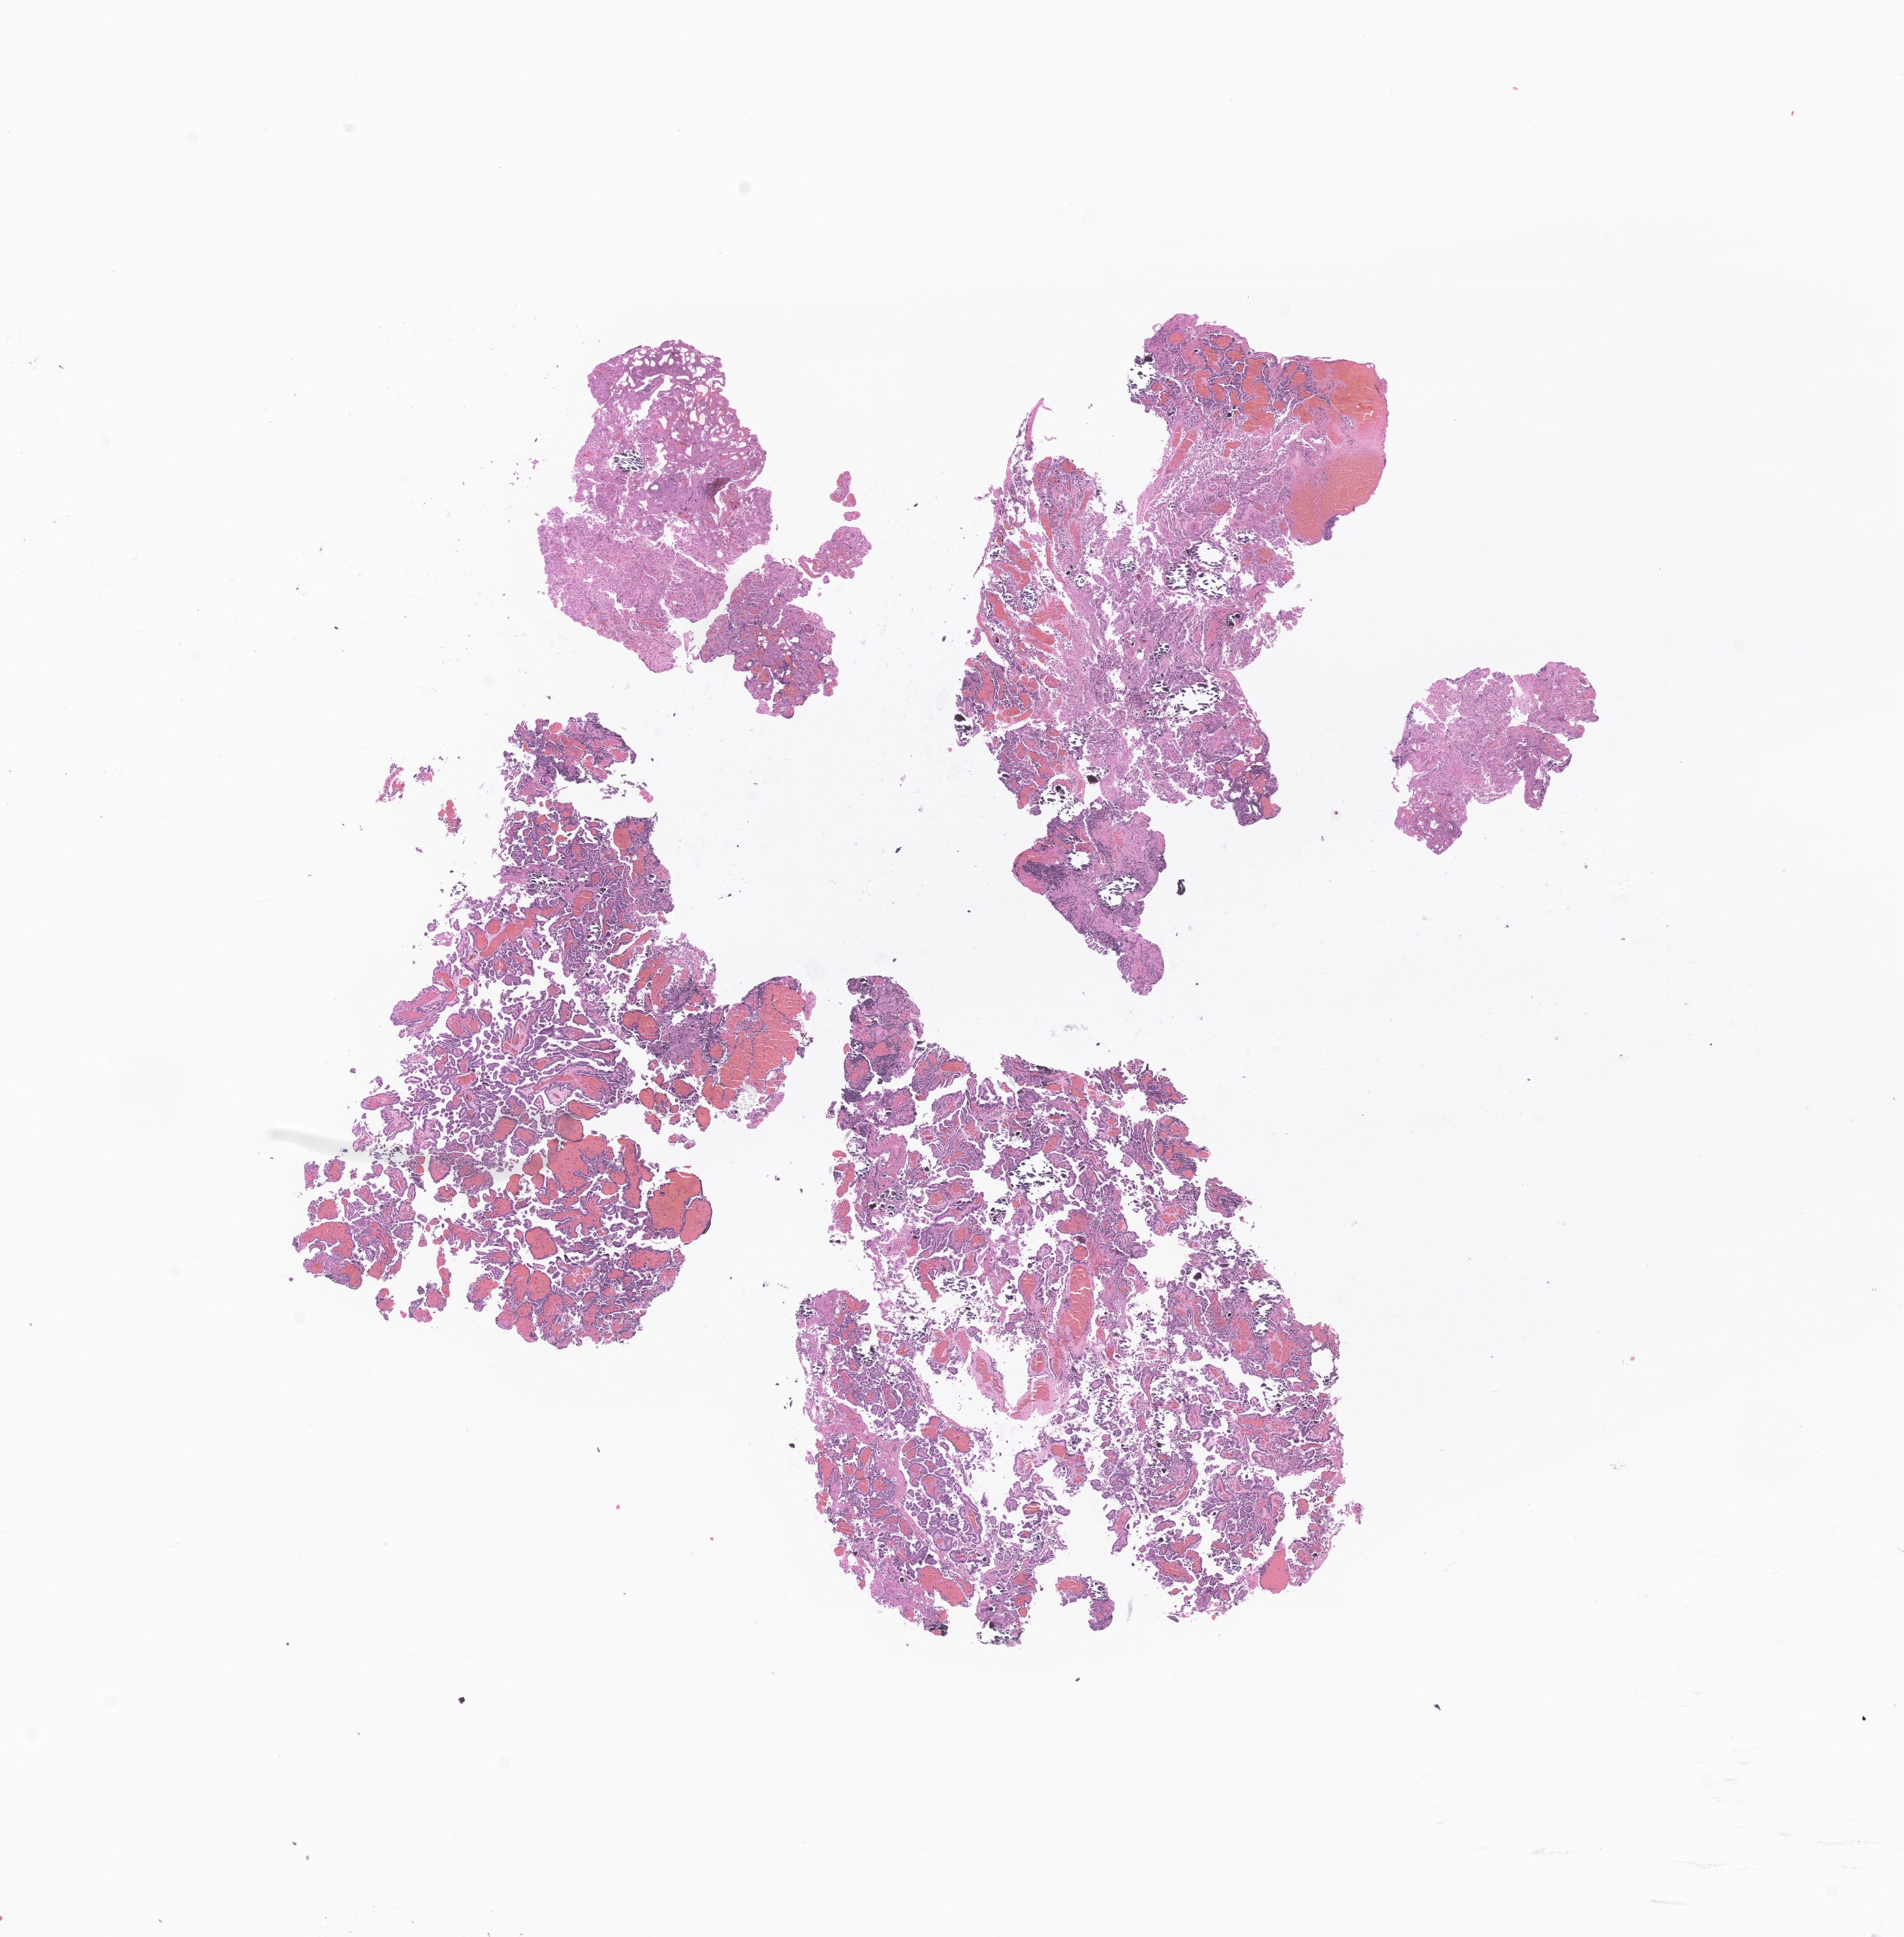
Digitized hematoxylin and eosin (H&E)-stained section of tumor tissue from the brain, shown as a low-resolution overview of the whole scanned area (about 12.3 x 12.5 mm). FFPE section. Patient: female, age 72 months (6 years).
- recorded diagnosis: Choroid plexus papilloma, NOS